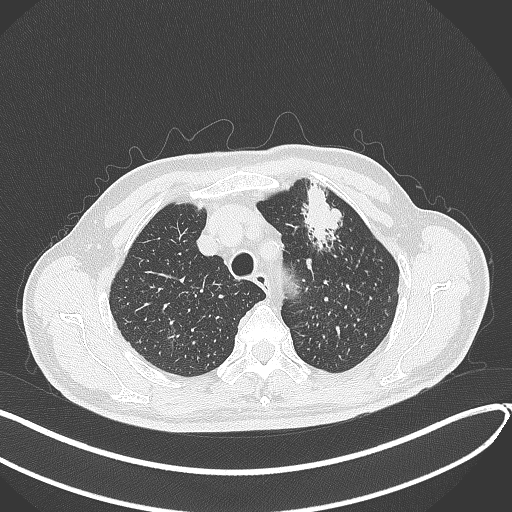
Chest CT, one axial slice. Position 341 of 459 along the scan axis. 120 kVp. Lung window (W 1500 / L -600 HU). 1 mm slice thickness. 512 × 512 image matrix. Male patient, age 74 years. From the clinical record (not read from this slice): clinical TNM (as recorded): T2b N0 M1c.
Structures marked on this image (rectangle marked by the reading radiologist):
- lung tumour (recorded histology: adenocarcinoma): bounding box (x1, y1, x2, y2) in pixels: (295, 183, 348, 255)